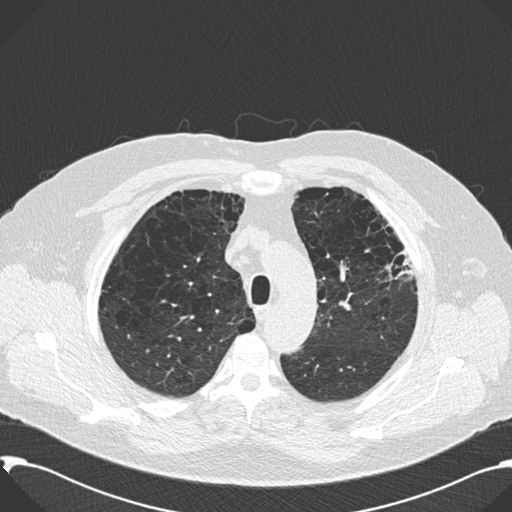
Axial slice from a low-dose chest CT screening exam. Second screening round (one year after baseline). Lung window (W 1500 / L -600 HU). Male participant, aged 59 years at enrolment. Current smoker at enrolment.
Lesion marked by an expert reader, box from (x=364, y=222) to (x=417, y=299) px. No non-calcified nodule or mass ≥4 mm was recorded by the screening reader at this exam.